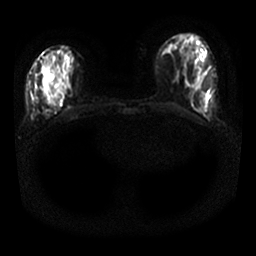
Breast MRI, one axial slice. Position 6 of 25 along the scan axis. Diffusion-weighted series; image 2 of 4 stored at this slice position (different b-values; order by instance number). 1.5 T. 4 mm slice thickness. 256 × 256 image matrix, field of view 330 × 330 mm. Female patient.
Outlined on this slice (outlined manually by an expert reader):
- tumour on diffusion-weighted imaging: bounding box (x1, y1, x2, y2) in pixels: (58, 87, 65, 98)